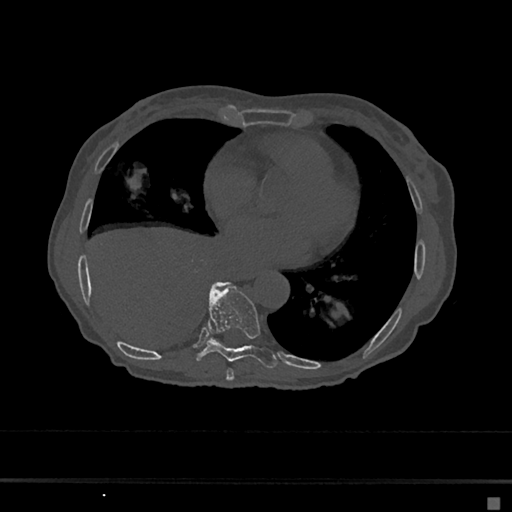
CT including the spine, one axial slice; position 320 of 797 along the scan axis; bone window (W 1800 / L 400 HU); 0.5 mm slice thickness; 512 × 512 image matrix, field of view 360 × 360 mm. Patient: female, 68 years. Case-level facts recorded for this patient, not image findings: primary cancer: renal.
Outlined on this slice (semi-automatically segmented with operator editing):
- T7 vertebra: bounding box (x1, y1, x2, y2) in pixels: (226, 368, 234, 381)
- T8 vertebra: (196, 282, 277, 369)
- T9 vertebra: (212, 282, 224, 341)